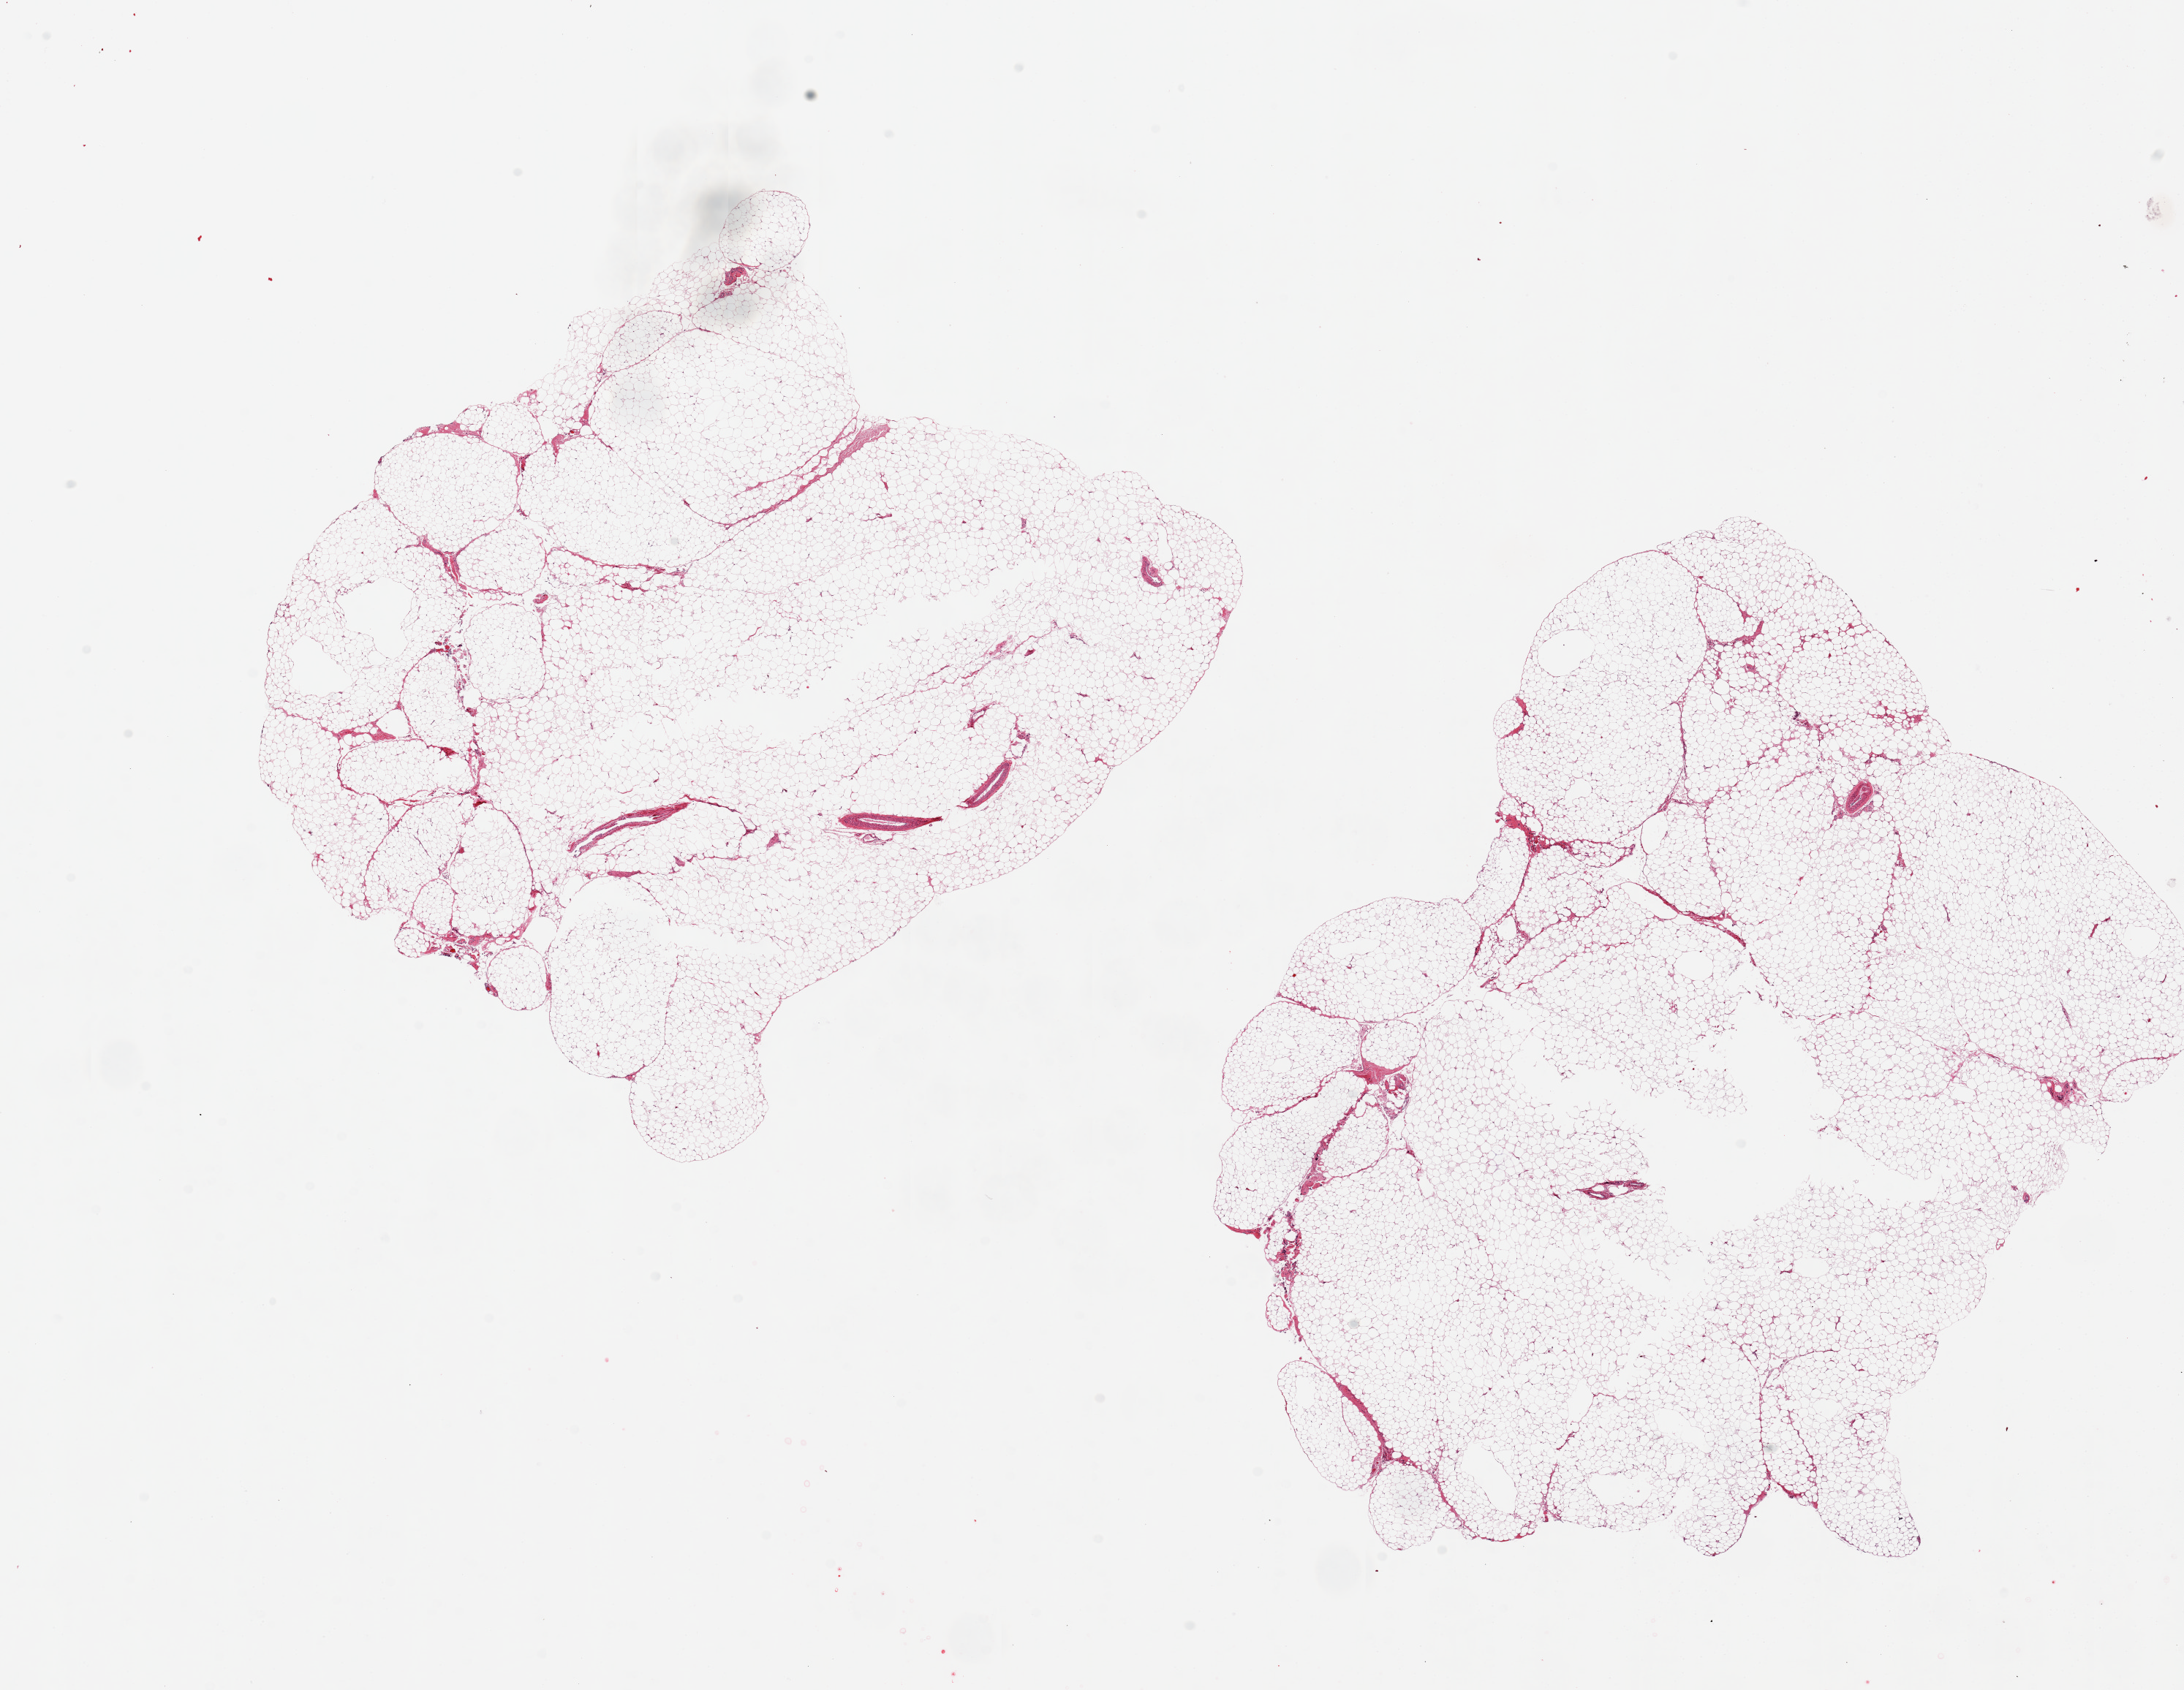
Hematoxylin and eosin (H&E) whole-slide image — shown as a low-resolution overview of the whole scanned area (about 23.6 x 18.3 mm, acquisition: 20x scan); PAXgene-fixed, paraffin-embedded tissue; target tissue: omentum; donor tissue sample. Donor: female.
Reviewer comment on this tissue sample: 2 pieces ~9x8mm.